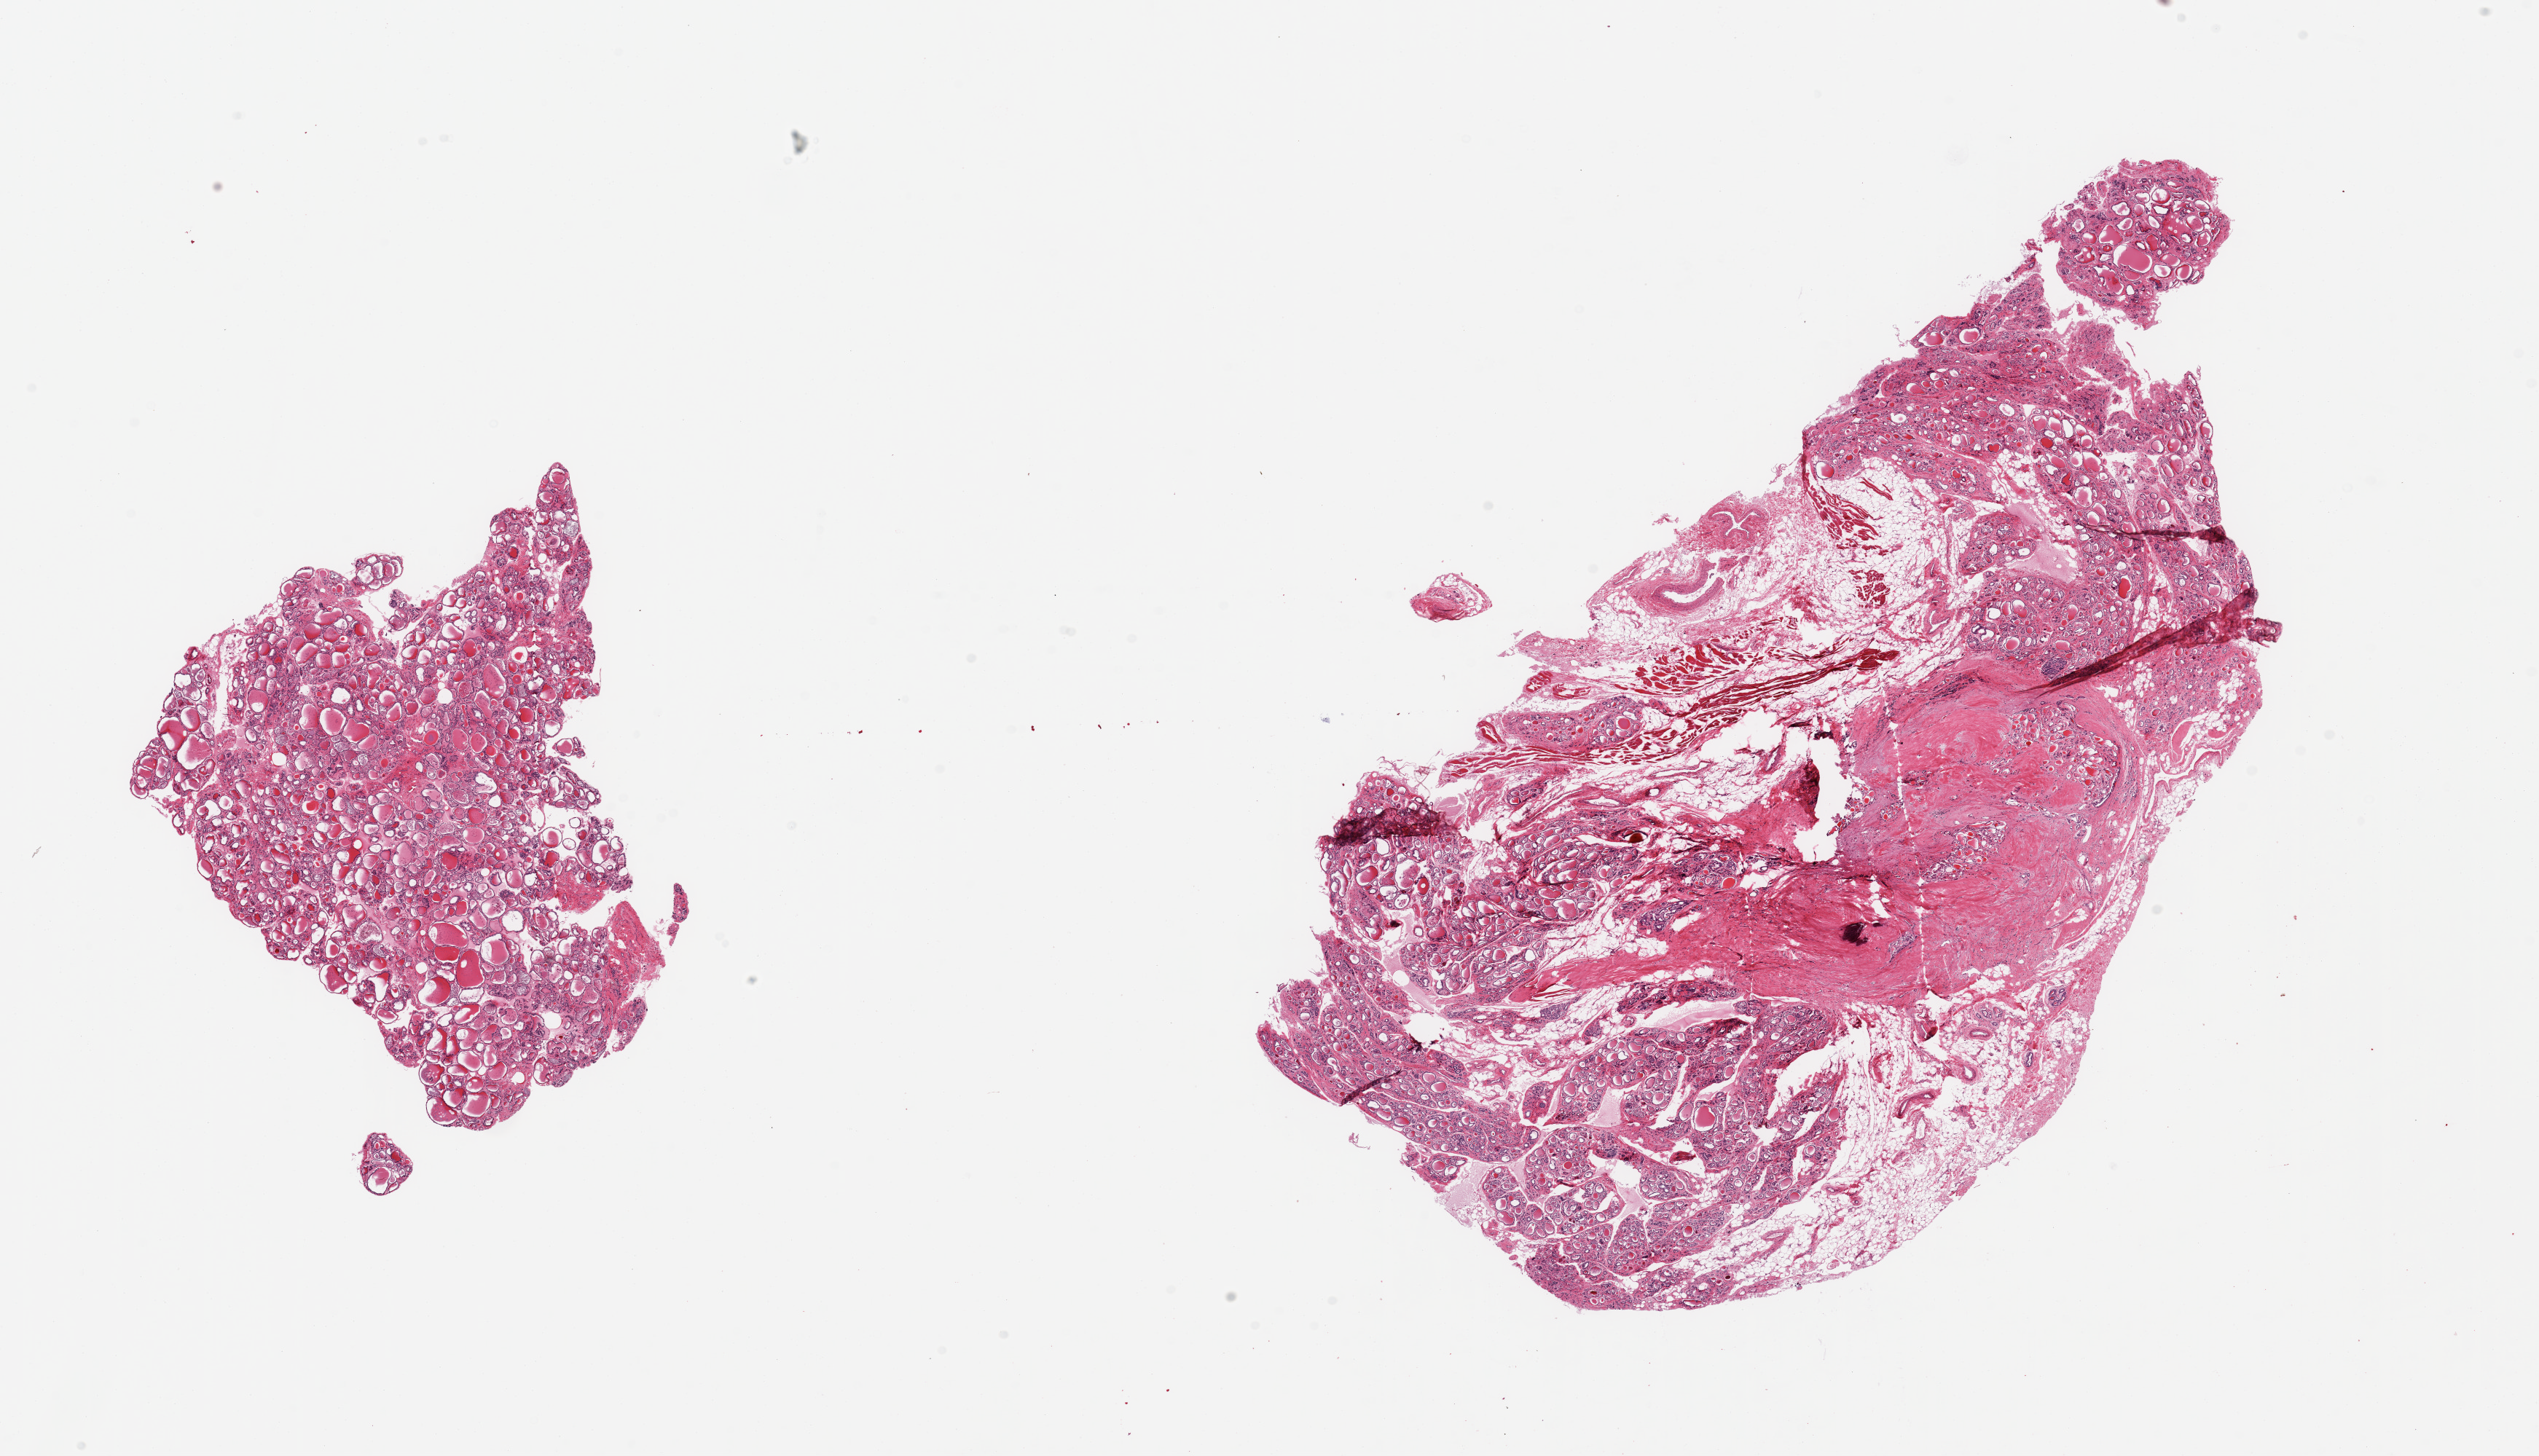
Digitized hematoxylin and eosin (H&E)-stained section, shown as a low-resolution overview of the whole scanned area (about 27.6 x 15.8 mm); PAXgene-fixed, paraffin-embedded tissue; sampled site (target tissue): thyroid; donor tissue sample. Donor: male.
- pathologist's review note for this sample: 2 pieces, 5mm calcifying adenomatoid nodule; Regressive changes